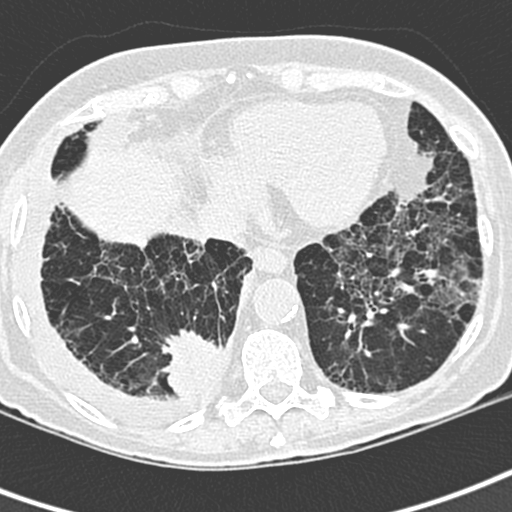
Low-dose screening chest CT, one axial slice; position 78 of 220 along the scan axis; lung window (W 1500 / L -600 HU); 1.3 mm slice thickness; 512 × 512 image matrix, field of view 288 × 288 mm.
Outlined on this slice (manually delineated by an expert):
- lesion 1 (tumor, lower lobe of right lung): bounding box [x1, y1, x2, y2] px = [162, 330, 223, 398]